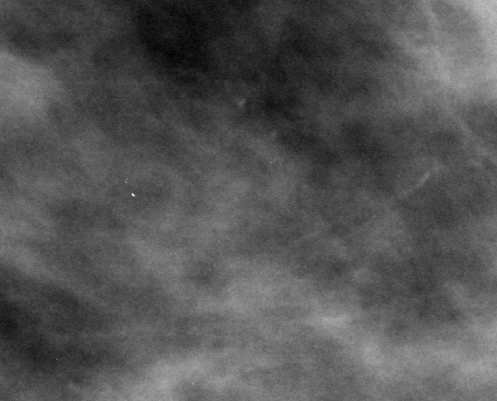
Region of interest cut from a scanned film mammogram (one marked finding); left breast; MLO view; BI-RADS breast density category 3 (scale 1–4).
Calcifications, morphology amorphous, distribution clustered; BI-RADS assessment category 4; subtlety rating 1 on a 1 (subtle) to 5 (obvious) scale; pathology result (as recorded, not read from the image): malignant.